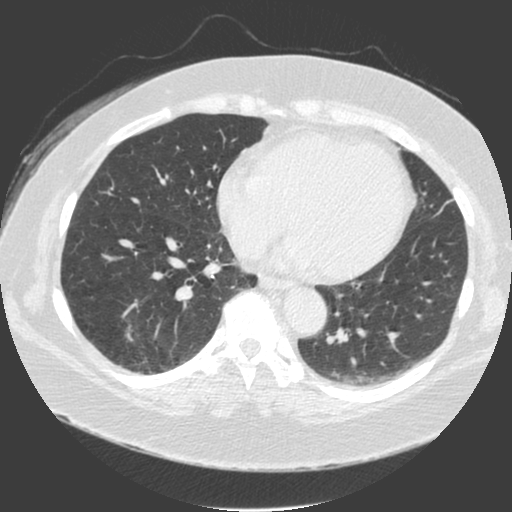
Axial slice from a low-dose chest CT screening exam; third screening round (two years after baseline); lung window (W 1500 / L -600 HU); 512 × 512 image matrix. Female participant, aged 56 years at enrolment.
- Lesion marked by an expert reader, bounding box [x1, y1, x2, y2] px = [94, 299, 155, 359].
- The screening reader recorded 4 non-calcified nodules or masses ≥4 mm on this exam (left lower lobe, right lower lobe, right lower lobe, right lower lobe); which of them this box marks is not recorded.
- Official screen result: positive, other.
- Participant outcome: lung cancer diagnosed 20 days after this screen — adenosquamous carcinoma, right lower lobe, poorly differentiated (G3), stage IA (AJCC 6th edition), 25 mm at pathology.